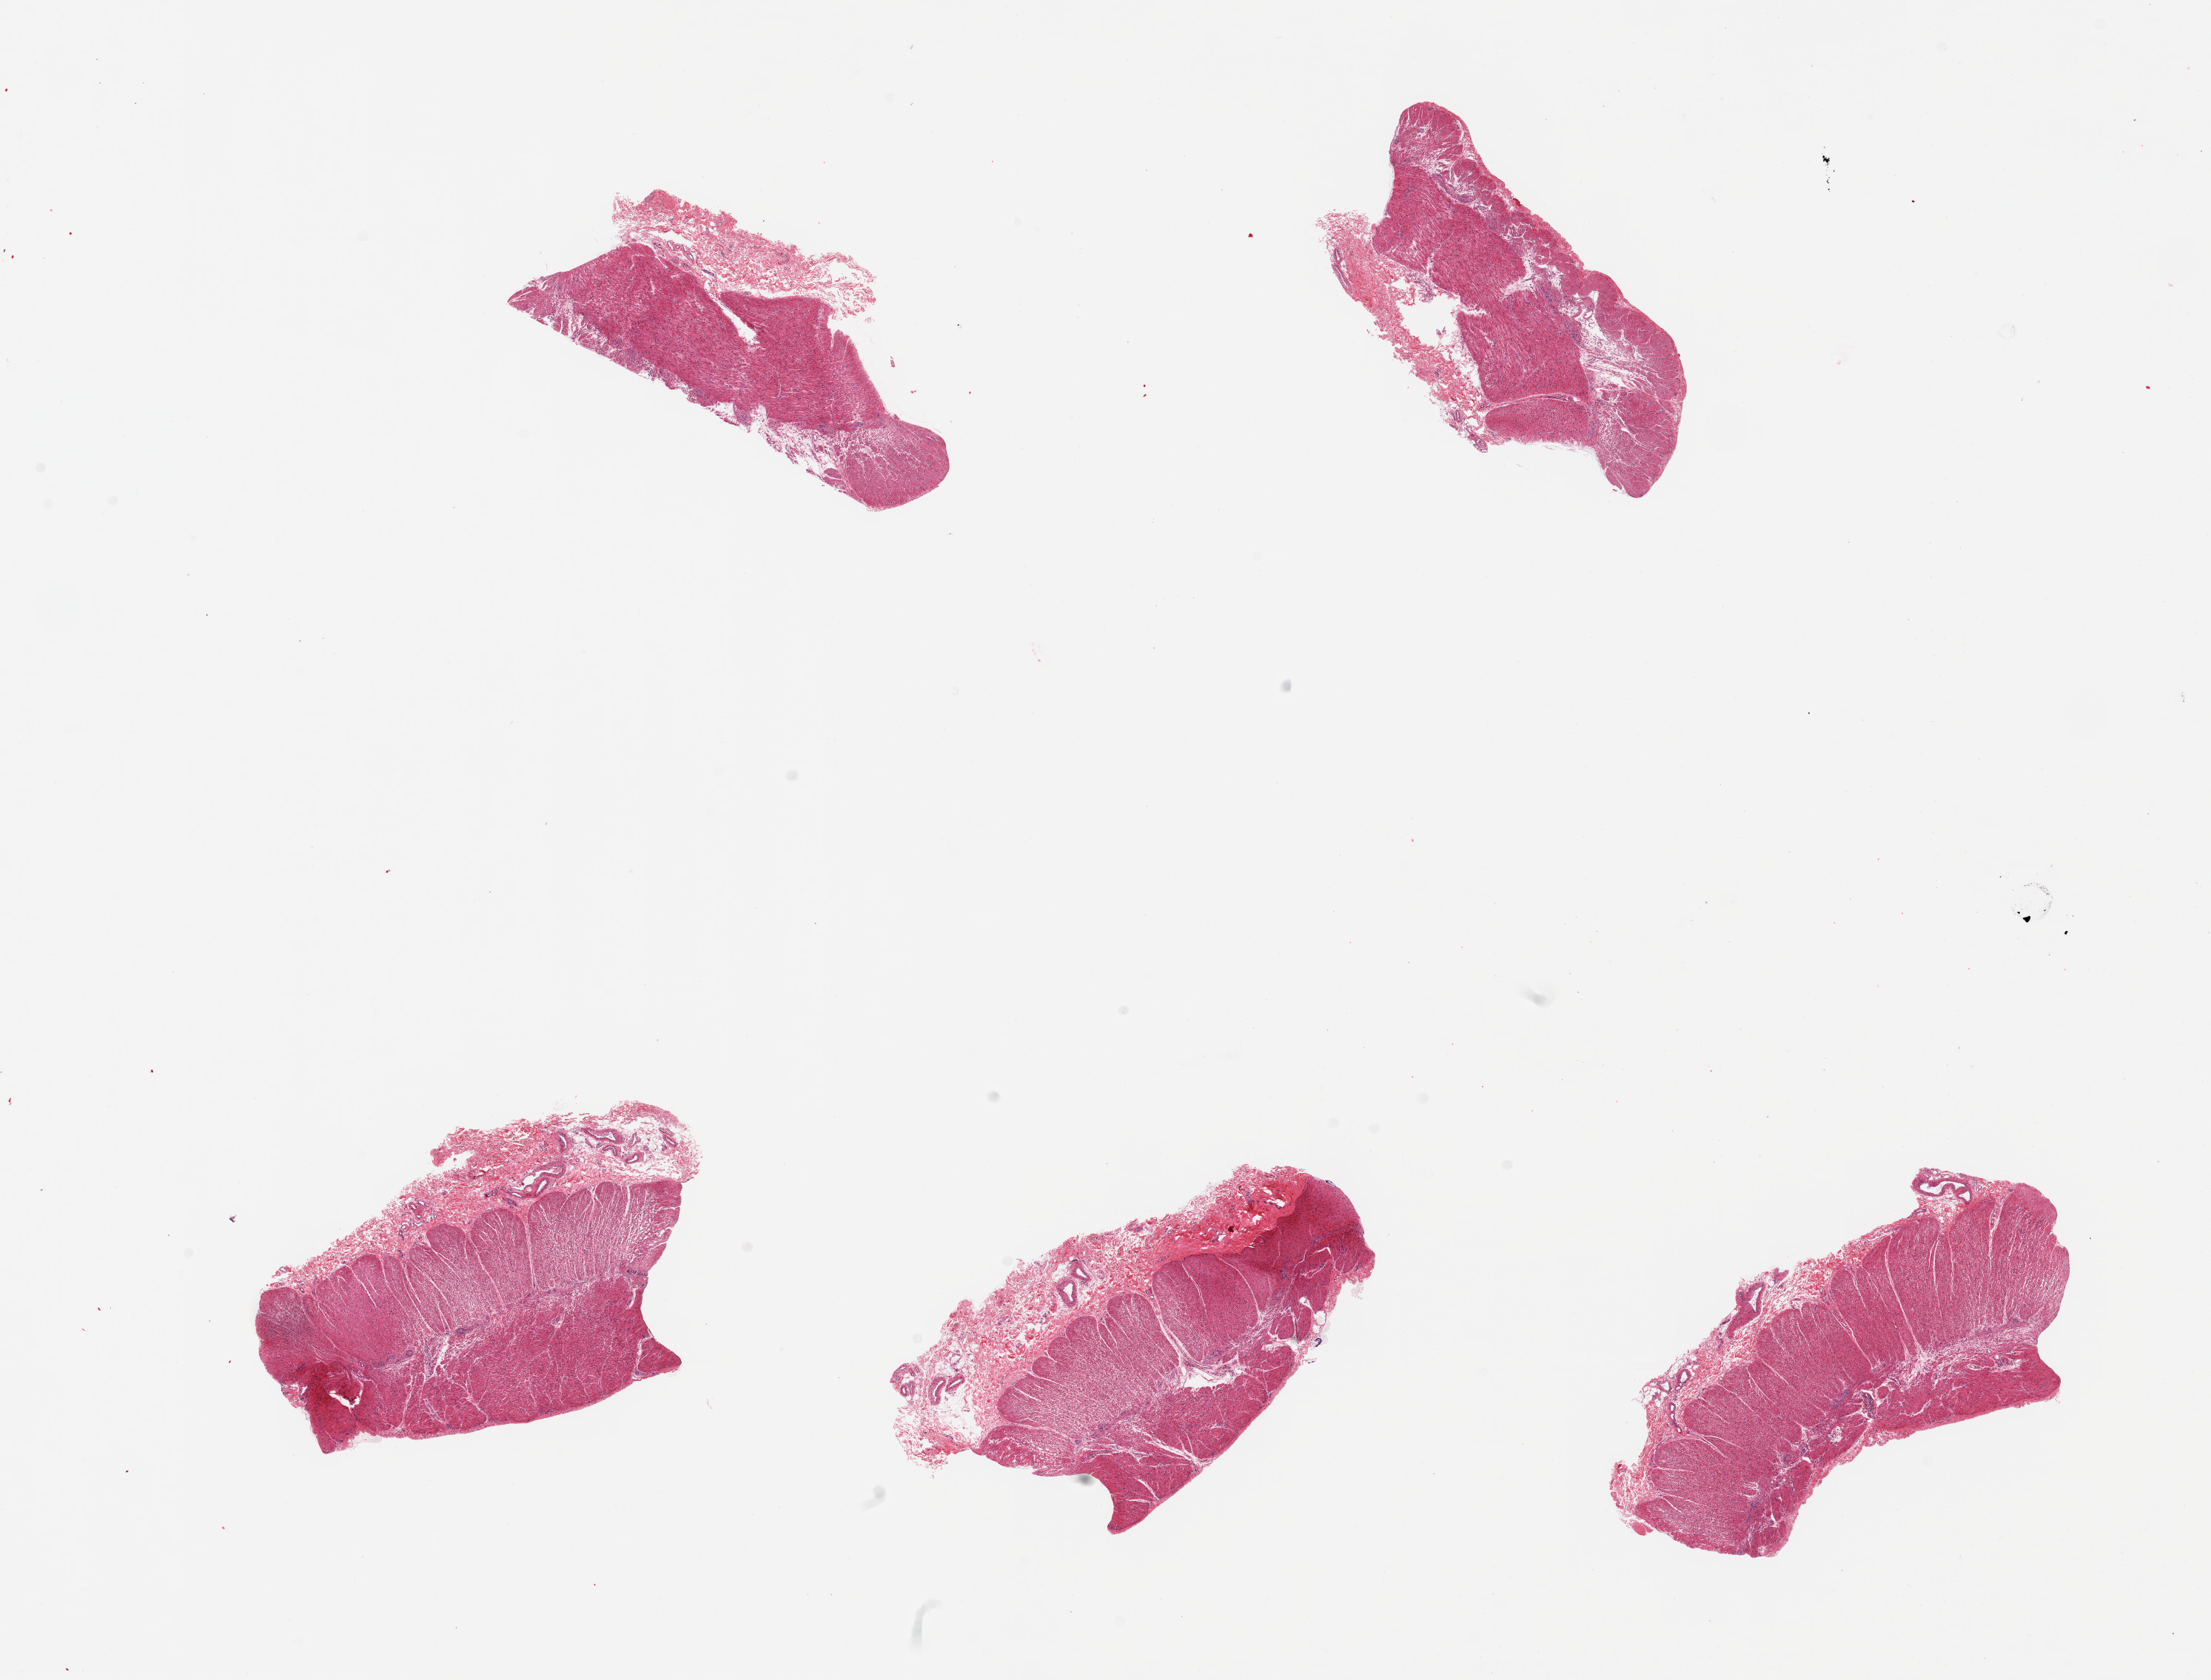
Whole-slide image, haematoxylin and eosin stain, low-resolution overview of the scanned area, about 23.6 x 18.0 mm (acquisition: 20x scan), PAXgene-fixed, paraffin-embedded tissue, sampled site (target tissue): sigmoid colon, tissue donor sample.
Reviewer comment on this tissue sample: 5 pieces; up to 0.8mm submucosa on each.